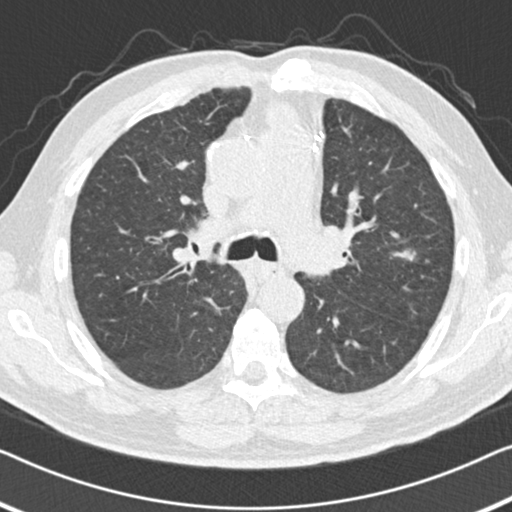
Low-dose screening chest CT, axial slice, first (baseline) screen, lung window (W 1500 / L -600 HU), 120 kVp, slice 56 of 155 in the series. Male, age 64 years at enrolment. Current smoker at enrolment.
- Expert-annotated lung lesion, bounding box [x1, y1, x2, y2] px = [381, 229, 439, 282].
- The screening reader recorded 2 non-calcified nodules or masses ≥4 mm on this exam (left upper lobe, right middle lobe); which of them this box marks is not recorded.
- Official screen result: positive, change unspecified: nodule(s) >= 4 mm or enlarging nodule(s), mass(es), or other non-specific abnormalities suspicious for lung cancer.
- Later outcome: lung cancer diagnosed 133 days after this screen — adenocarcinoma, NOS, left upper lobe, poorly differentiated (G3), stage IA (AJCC 6th edition), 15 mm at pathology.